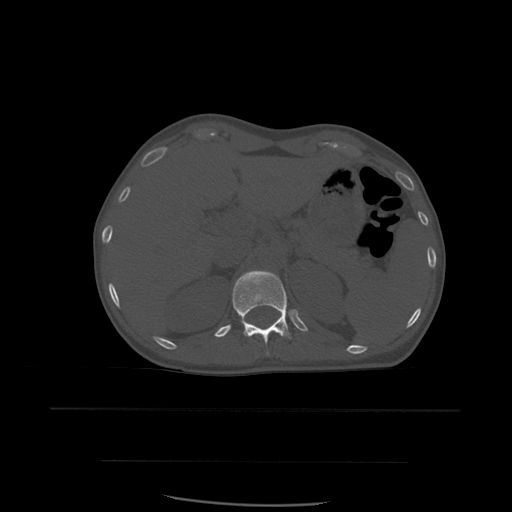
CT including the spine, one axial slice. Position 273 of 574 along the scan axis. Bone window (W 1800 / L 400 HU). 1.25 mm slice thickness. 512 × 512 image matrix, field of view 392 × 392 mm. Patient age 48 years. Case-level facts recorded for this patient, not image findings: primary cancer: lung; vertebrae with lytic lesions (as recorded): T11.
Annotated regions visible in this slice (semi-automatically segmented with operator editing):
- T12 vertebra: bounding box <233,270,292,354> (left, top, right, bottom; pixels)